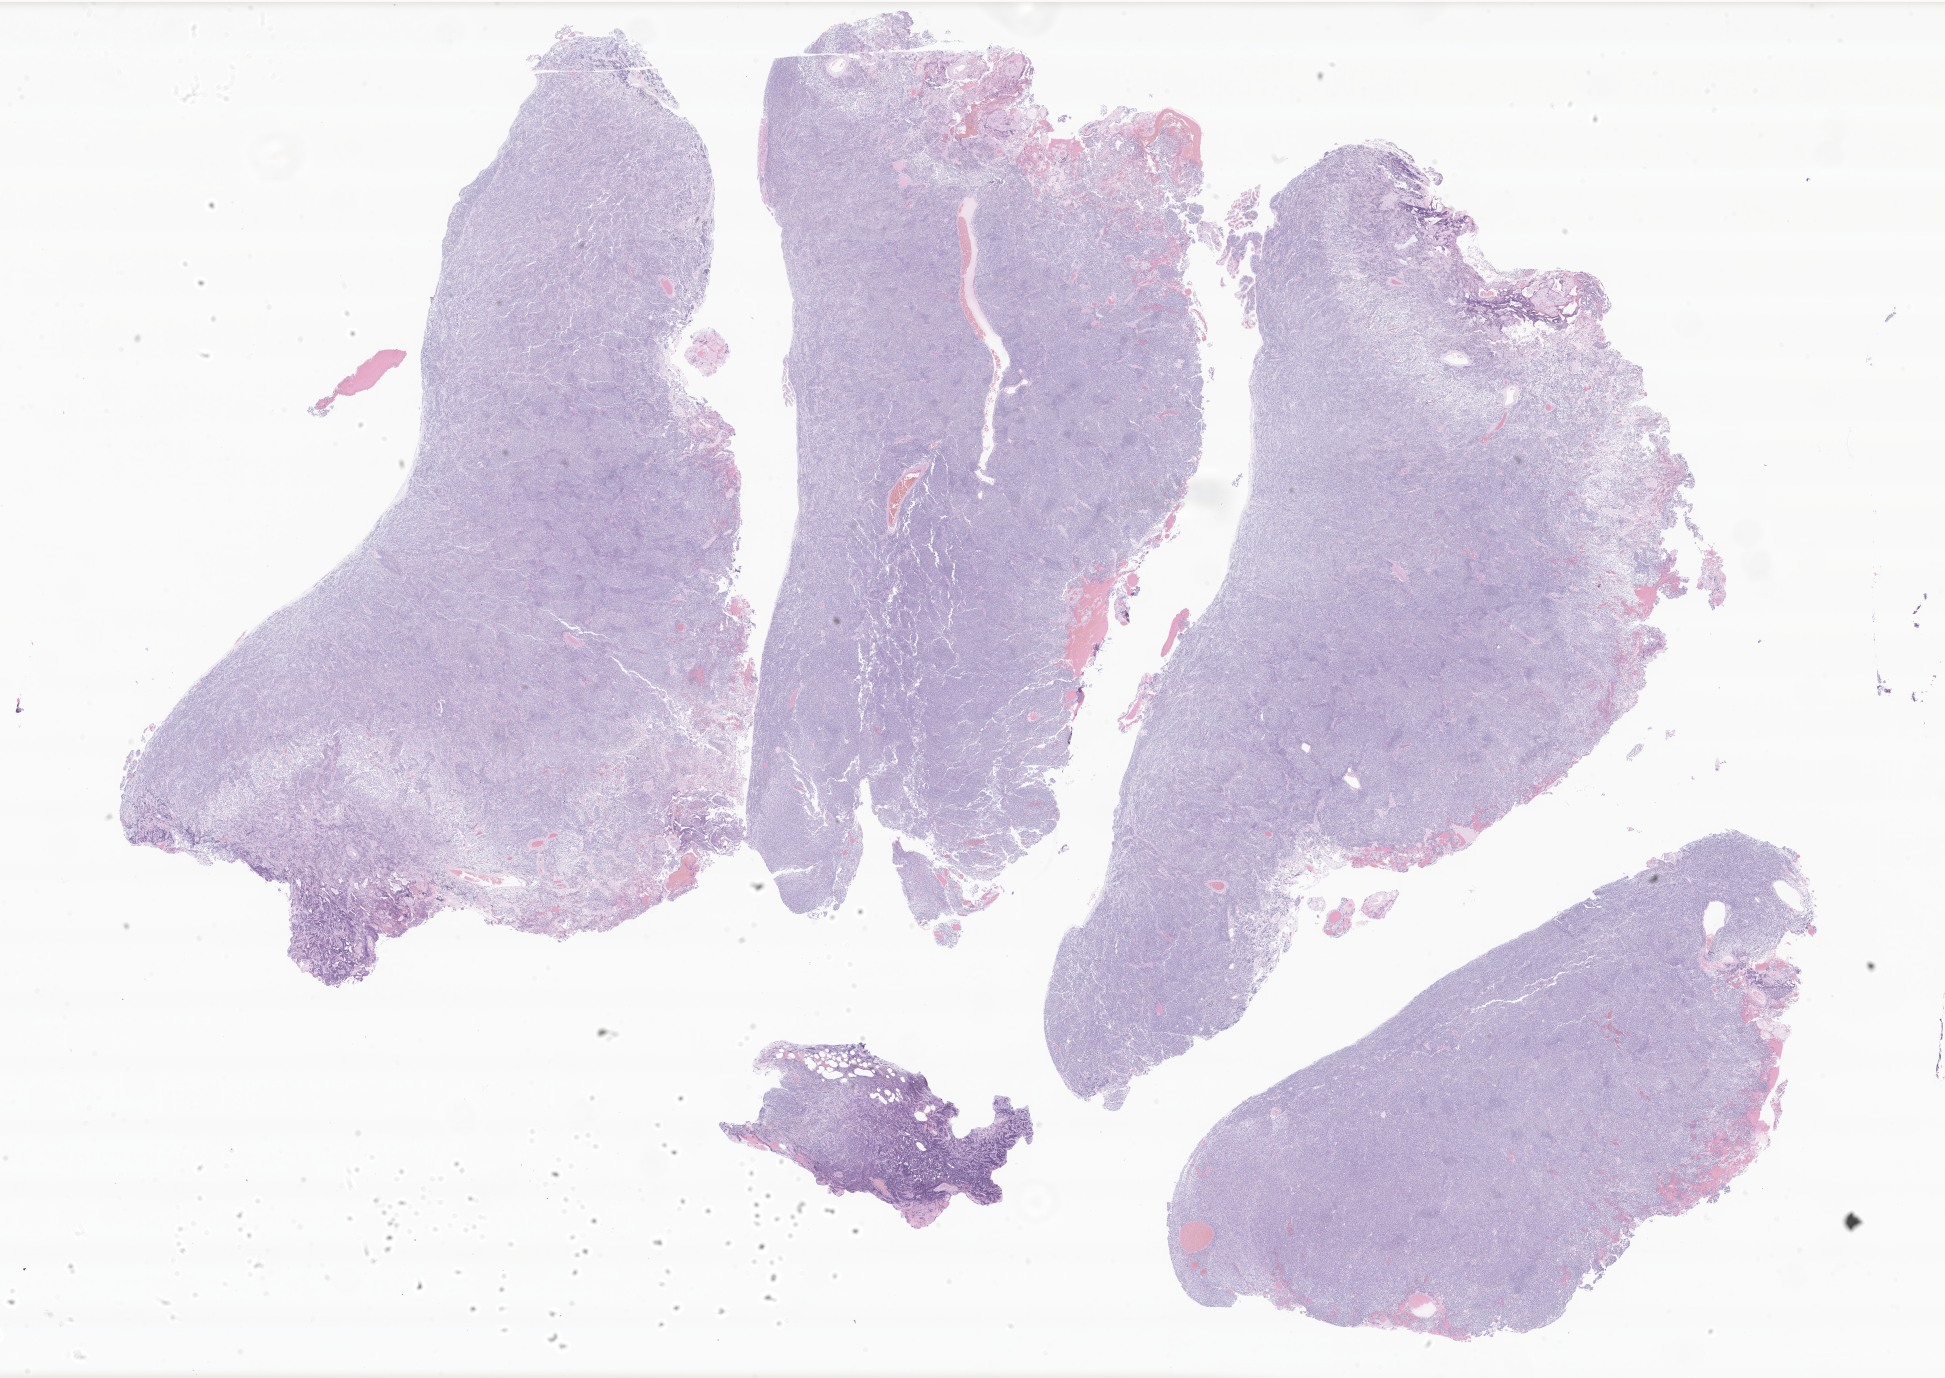
Digitized haematoxylin and eosin-stained section of tumor tissue from the brain — low-resolution overview of the scanned area, about 32.8 x 23.2 mm. FFPE section. Patient: male, age 79 months (6 years 7 months).
• diagnosis: Medulloblastoma, NOS